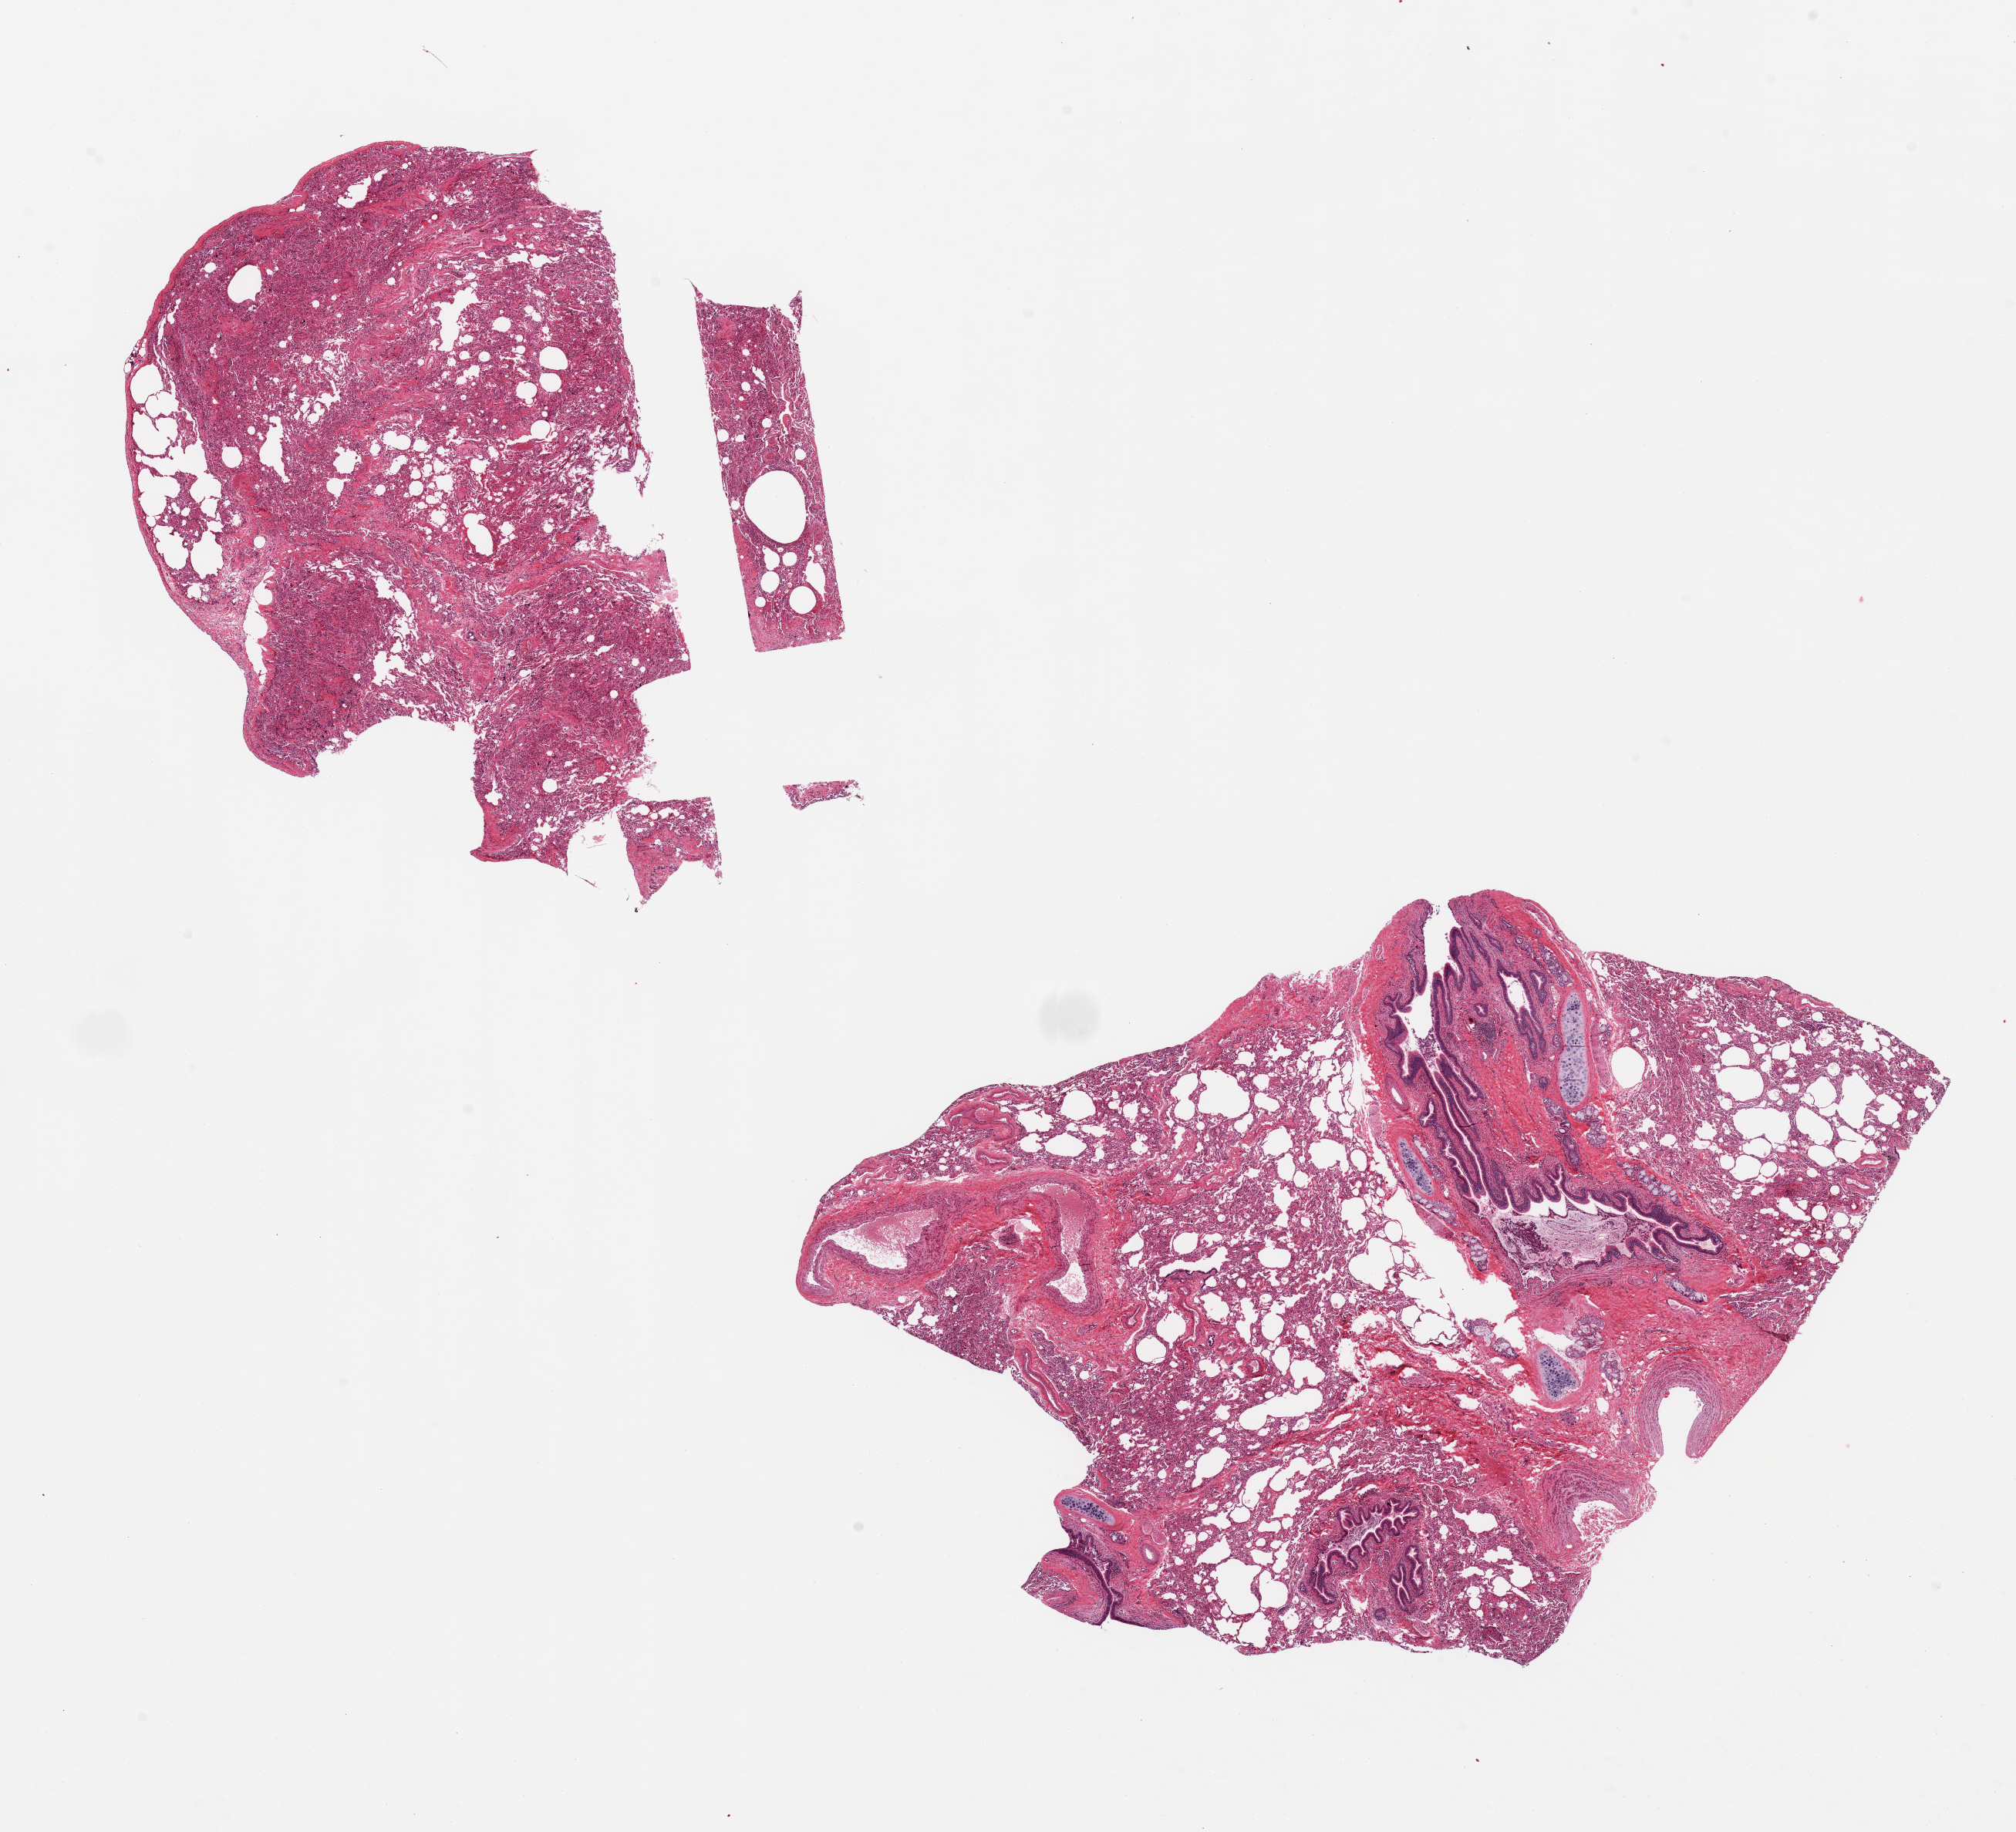
Digitized haematoxylin and eosin-stained section, brightfield, whole scanned area (about 20.7 x 18.8 mm) shown as a low-resolution overview. PAXgene-fixed, paraffin-embedded tissue. Sampled site (target tissue): lung. Tissue donor sample.
Review note (as recorded): 2 pieces 12x8 & 7x5 mm; patchy atelectasis.